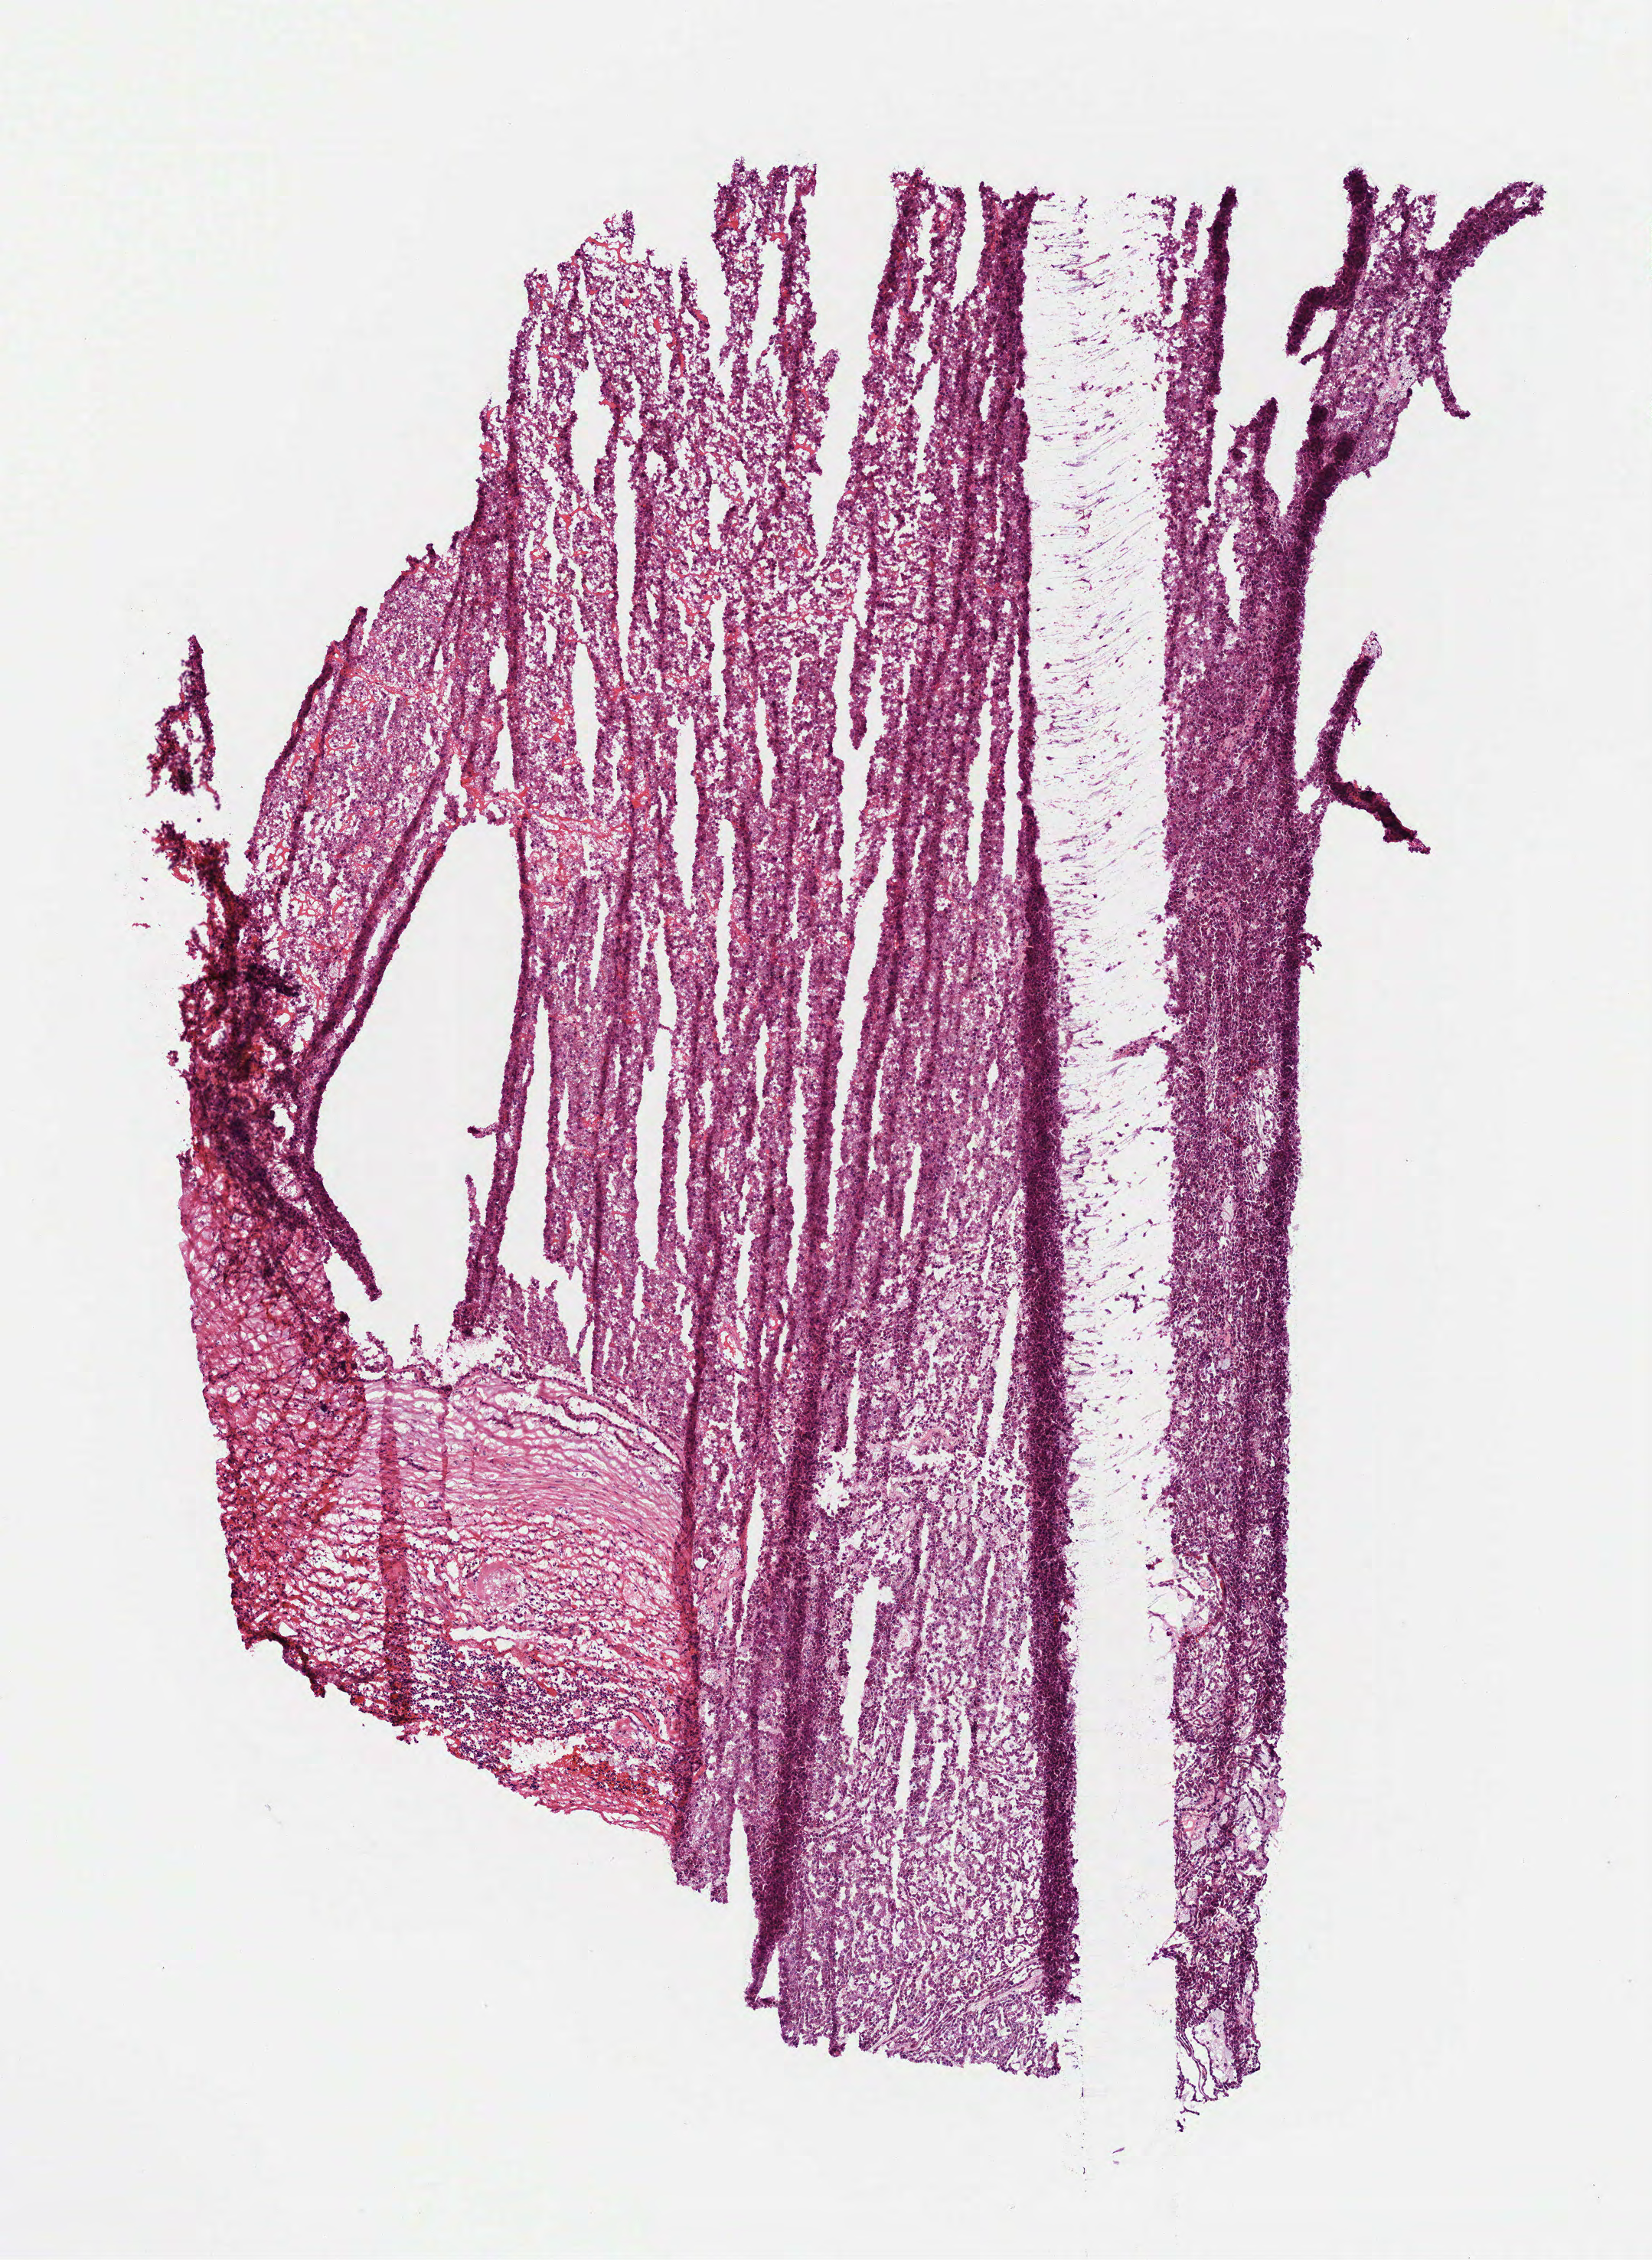
Digitized H&E-stained tissue section (whole slide), shown as a low-resolution overview of the whole scanned area (about 4.4 x 6.0 mm), frozen section from the bottom of the tissue portion, primary tumour sample from the kidney. Patient: male, age at initial diagnosis 59 years. Slide review estimates, as recorded: tumour cells 88%, tumour nuclei 80%, normal cells 0%, stromal cells 12%, necrosis 0%.
AJCC pathologic stage: I. Laterality: left. Histologic diagnosis: Papillary adenocarcinoma, NOS.